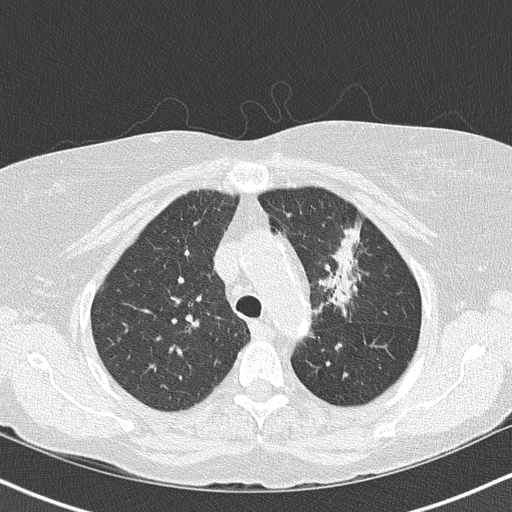
Chest CT (low-dose screening protocol), one axial image, third annual screen, lung window (W 1500 / L -600 HU), 2 mm slice thickness, 512 × 512 image matrix, field of view 320 × 320 mm. Female participant, aged 68 years at enrolment. Former smoker at enrolment.
Expert-annotated lung lesion, box from (x=300, y=211) to (x=382, y=319) px. The exam's reader record, not a measurement of the box and not confirmed to be the same lesion: non-calcified nodule or mass ≥4 mm, left upper lobe, 5 × 5 mm, poorly defined margins, mixed attenuation, pre-existing on the prior screen: yes; interval growth: yes. Official screen result: positive, other. Later outcome: lung cancer diagnosed 42 days after this screen — adenocarcinoma, NOS, left upper lobe, poorly differentiated (G3), stage IB (AJCC 6th edition), 50 mm at pathology.